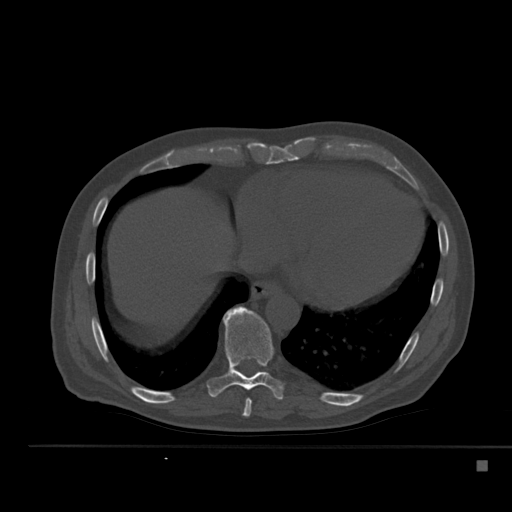
CT including the spine, one axial slice. Position 289 of 517 along the scan axis. Bone window (W 1800 / L 400 HU). 1.5 mm slice thickness. 512 × 512 image matrix, field of view 408 × 408 mm. Patient: male, 70 years. From the clinical record (not read from this slice): primary cancer: renal.
Annotated regions visible in this slice (semi-automatically segmented with operator editing):
- T8 vertebra: box from (x=242, y=398) to (x=252, y=417) px
- T9 vertebra: (x=207, y=306)–(x=284, y=400)